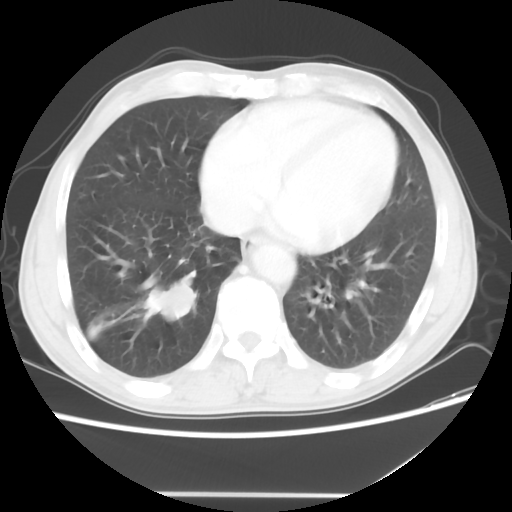
Chest CT, one axial slice. Slice 17 of 56 in the series (ordered by position). Reconstruction kernel STANDARD. Lung window (W 1500 / L -600 HU). 5 mm slice thickness. 512 × 512 image matrix. Patient: male, 65 years. From the clinical record (not read from this slice): clinical TNM (as recorded): T1c N3 M0; histopathological grade: G3.
Outlined on this slice (bounding box drawn by a radiologist):
- lung tumour (recorded histology: small cell carcinoma): box from (x=141, y=274) to (x=199, y=324) px